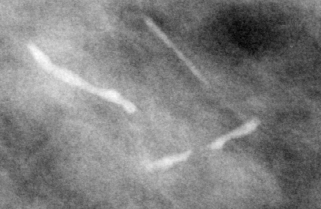
Region of interest cut from a scanned film mammogram (one marked finding), left breast, MLO view, BI-RADS breast density category 3 (scale 1–4).
Finding: calcifications, morphology large rodlike / round and regular, distribution regional; BI-RADS assessment category 2; benign without callback (not worked up further).